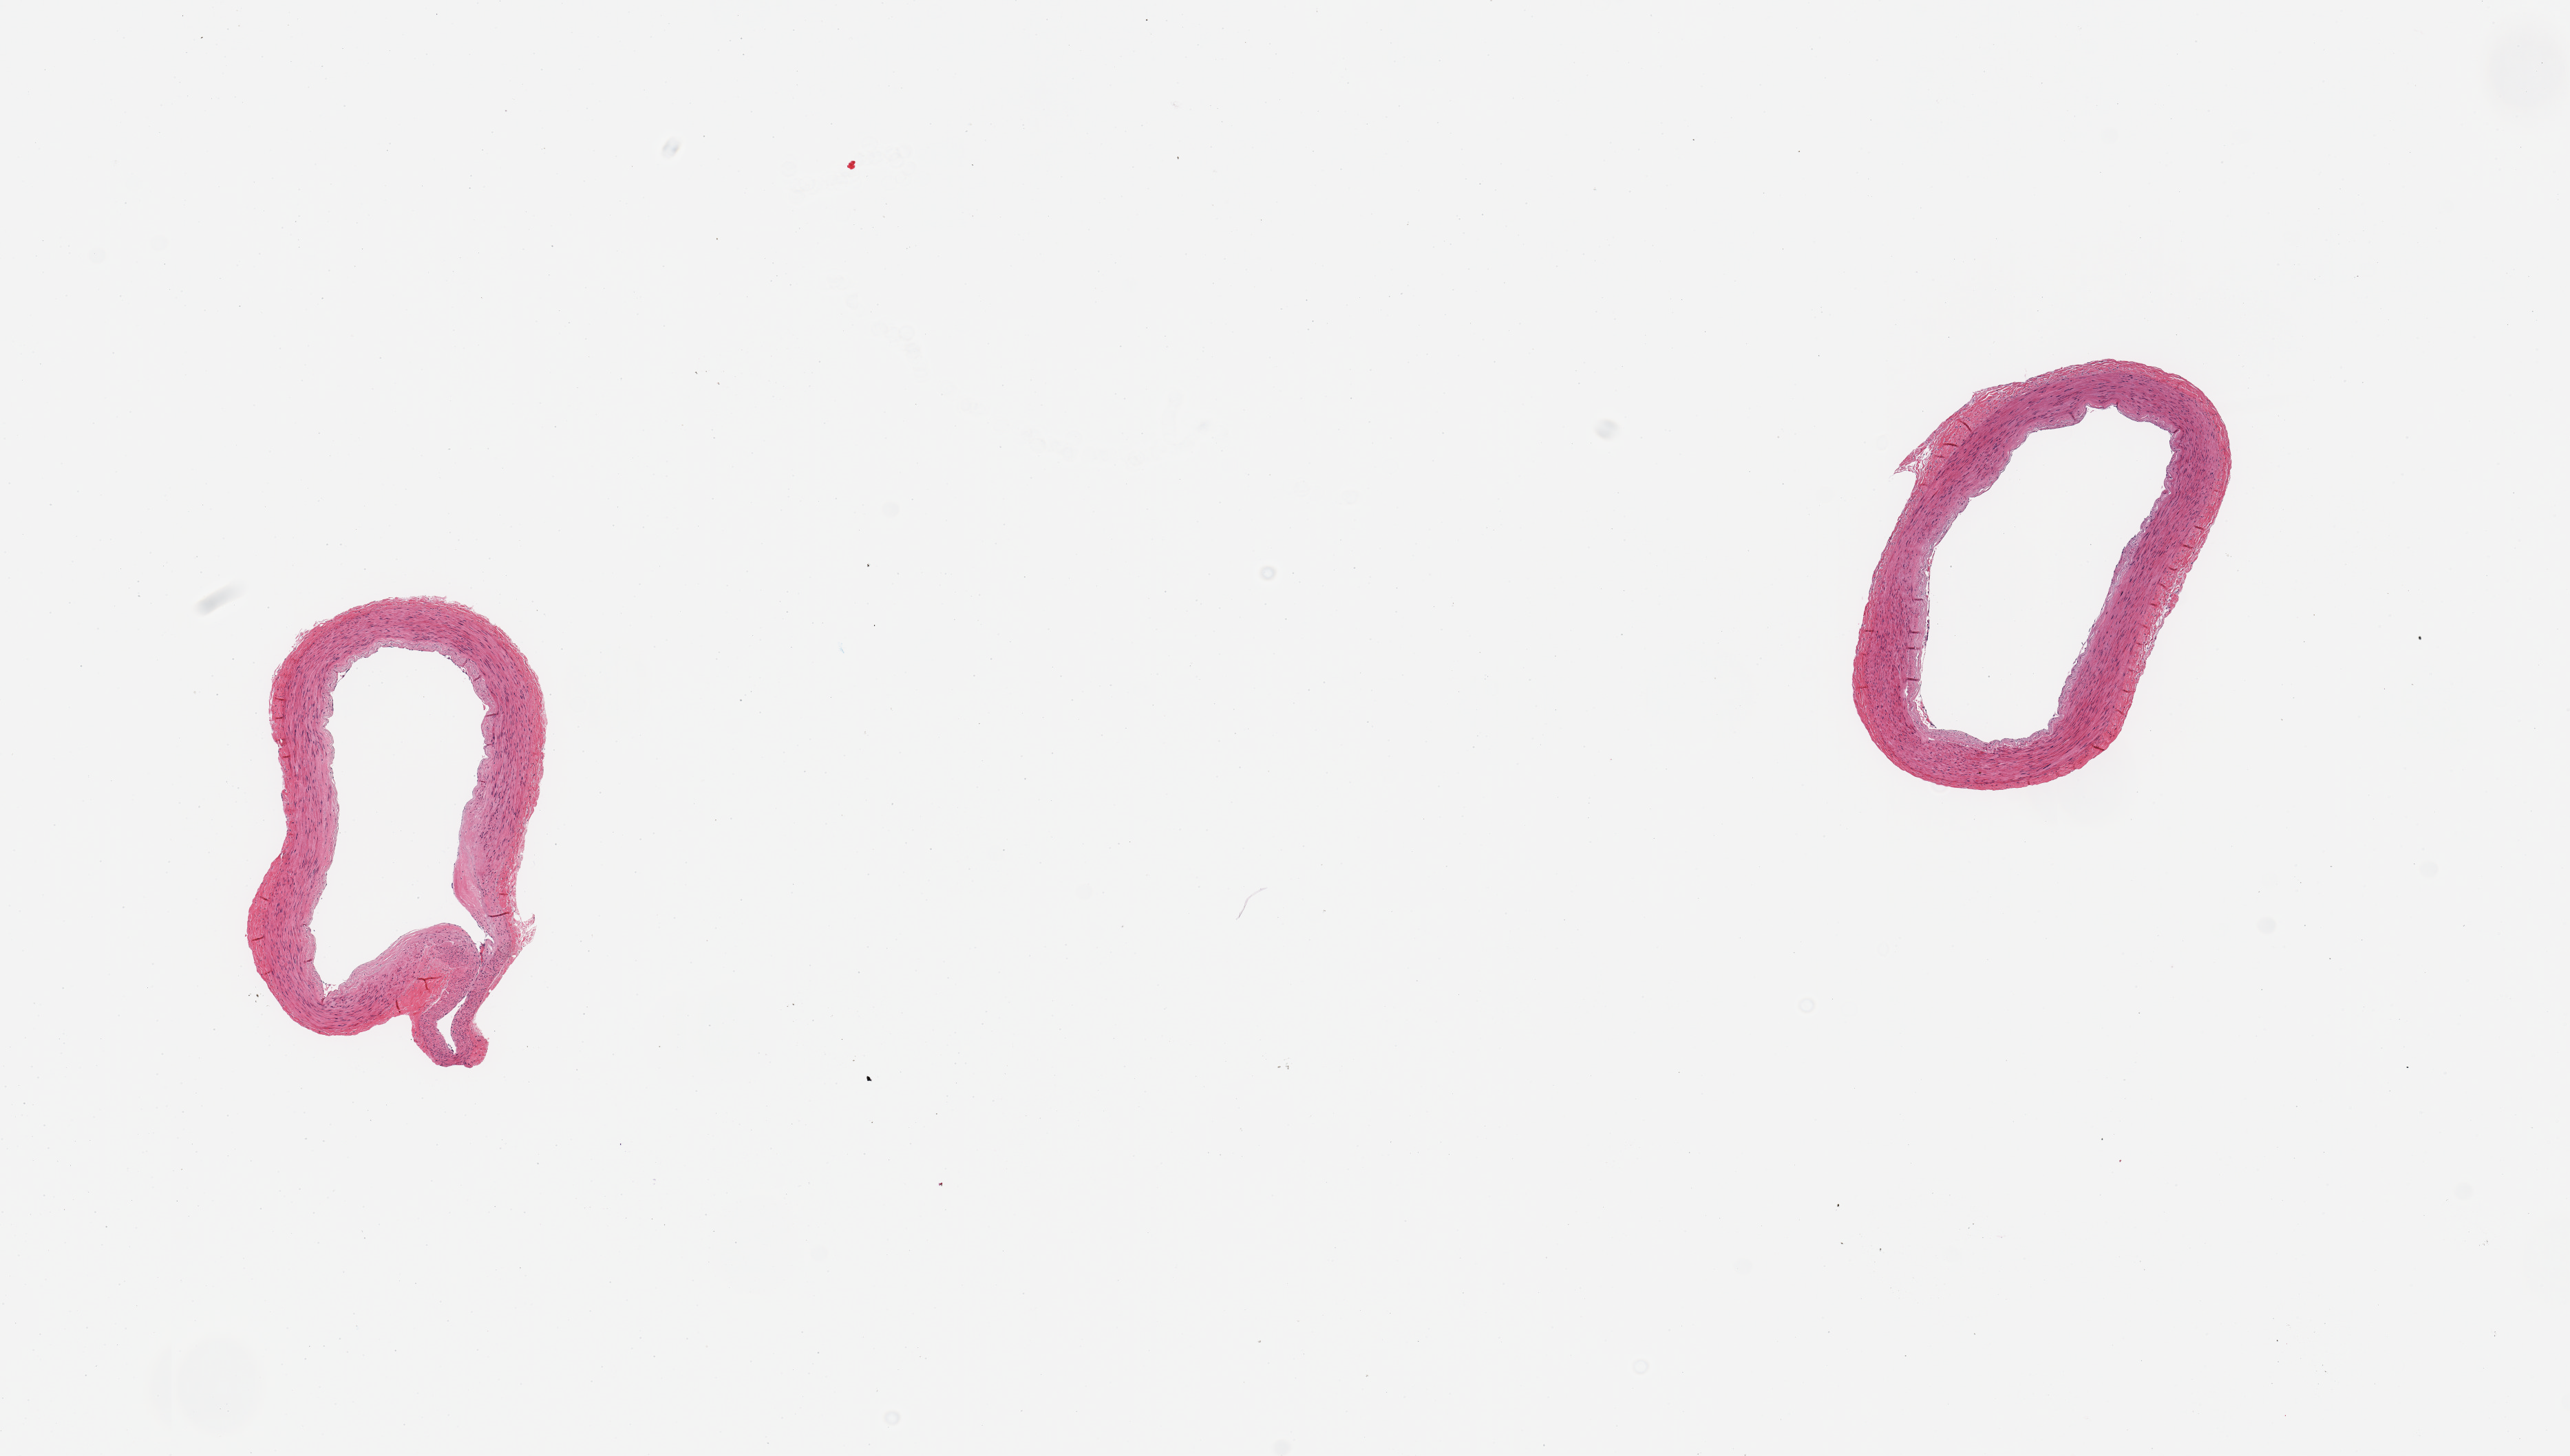
H&E whole-slide image, brightfield — shown as a low-resolution overview of the whole scanned area (about 14.8 x 8.4 mm, from a 20x scan), PAXgene-fixed paraffin-embedded (PFPE) section, section of tibial artery (target tissue), tissue donor sample.
Pathologist's review note for this sample: 2 pieces, no adherent fat or atherosis.